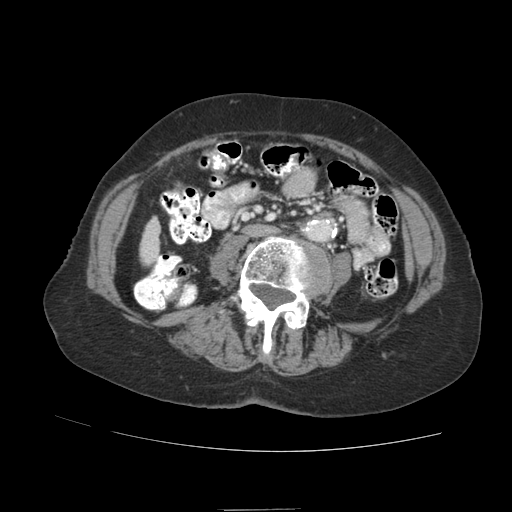
Contrast-enhanced abdominal CT (liver protocol), one axial slice; position 8 of 89 along the scan axis; 140 kVp; soft-tissue window (W 400 / L 40 HU); 2.5 mm slice thickness; 512 × 512 image matrix, field of view 360 × 360 mm. Case-level facts recorded for this patient, not image findings: diagnosis: hepatocellular carcinoma (patient treated with transarterial chemoembolisation; whether this scan precedes or follows treatment is not stated here); TNM stage (as recorded): Stage-II; Child-Pugh class: A; tumour nodularity: multinodular; tumour size: 4 cm.
Structures marked on this image (semi-automatically segmented with operator editing):
- liver parenchyma outside the tumour (the mass and vessels are separate outlines, so this box may not span the whole liver): bounding box (x1, y1, x2, y2) in pixels: (140, 216, 160, 264)